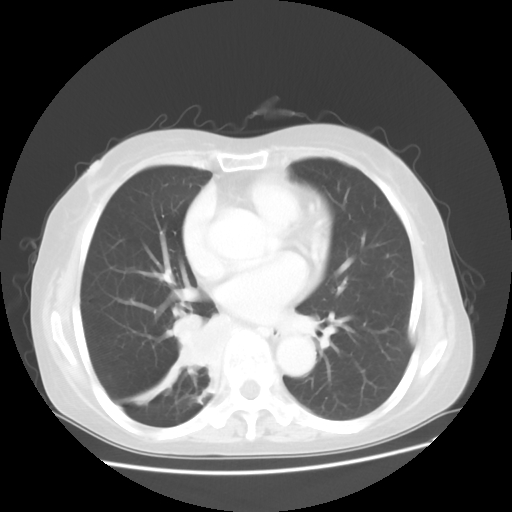
Chest CT, one axial slice. Position 21 of 48 along the scan axis. Lung window (W 1500 / L -600 HU). 5 mm slice thickness. 512 × 512 image matrix, field of view 360 × 360 mm. Female patient, age 63 years. From the clinical record (not read from this slice): clinical TNM (as recorded): T2 N3 M1b; histopathological grade: G3.
Structures marked on this image (rectangle marked by the reading radiologist):
- lung tumour (recorded histology: small cell carcinoma): box from (x=172, y=306) to (x=225, y=370) px